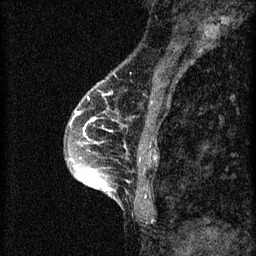
Breast MRI (dynamic contrast-enhanced), one sagittal slice; position 21 of 60 along the scan axis; 3 images stored at this slice position (order not interpretable as contrast timing); 1.5 T; TE 4.2 ms, TR 8.2 ms; 2 mm slice thickness; 256 × 256 image matrix. Female patient, age 45 years.
Structures marked on this image (semi-automatically segmented with operator editing):
- analysis volume of interest (the breast-tissue region the enhancement analysis was run in; not a lesion): bounding box (x1, y1, x2, y2) in pixels: (66, 104, 159, 217)
- tumour enhancement mask (voxels above the 70 % enhancement threshold inside the analysis volume of interest): (70, 112, 113, 195)